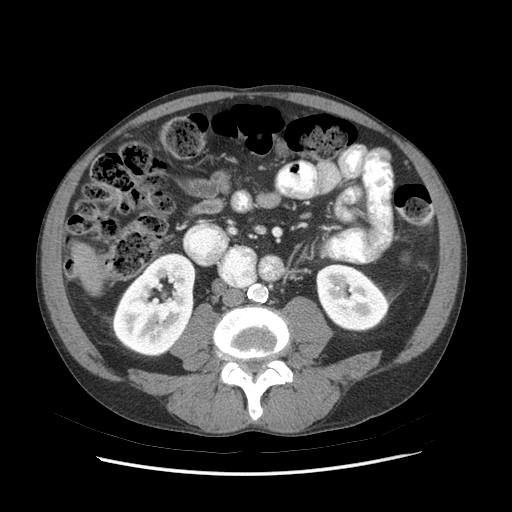
Contrast-enhanced abdominal CT (liver protocol), one axial slice; position 10 of 89 along the scan axis; reconstruction kernel STANDARD; 140 kVp; soft-tissue window (W 400 / L 40 HU); 2.5 mm slice thickness; 512 × 512 image matrix, field of view 380 × 380 mm. From the clinical record (not read from this slice): diagnosis: hepatocellular carcinoma (patient treated with transarterial chemoembolisation; whether this scan precedes or follows treatment is not stated here); TNM stage (as recorded): Stage-IIIB; Child-Pugh class: A; tumour differentiation: moderately differentiated; tumour nodularity: multinodular.
Outlined on this slice (semi-automatic segmentation, software-assisted and operator-edited):
- liver parenchyma outside the tumour (the mass and vessels are separate outlines, so this box may not span the whole liver): bounding box [x1, y1, x2, y2] px = [72, 246, 100, 290]